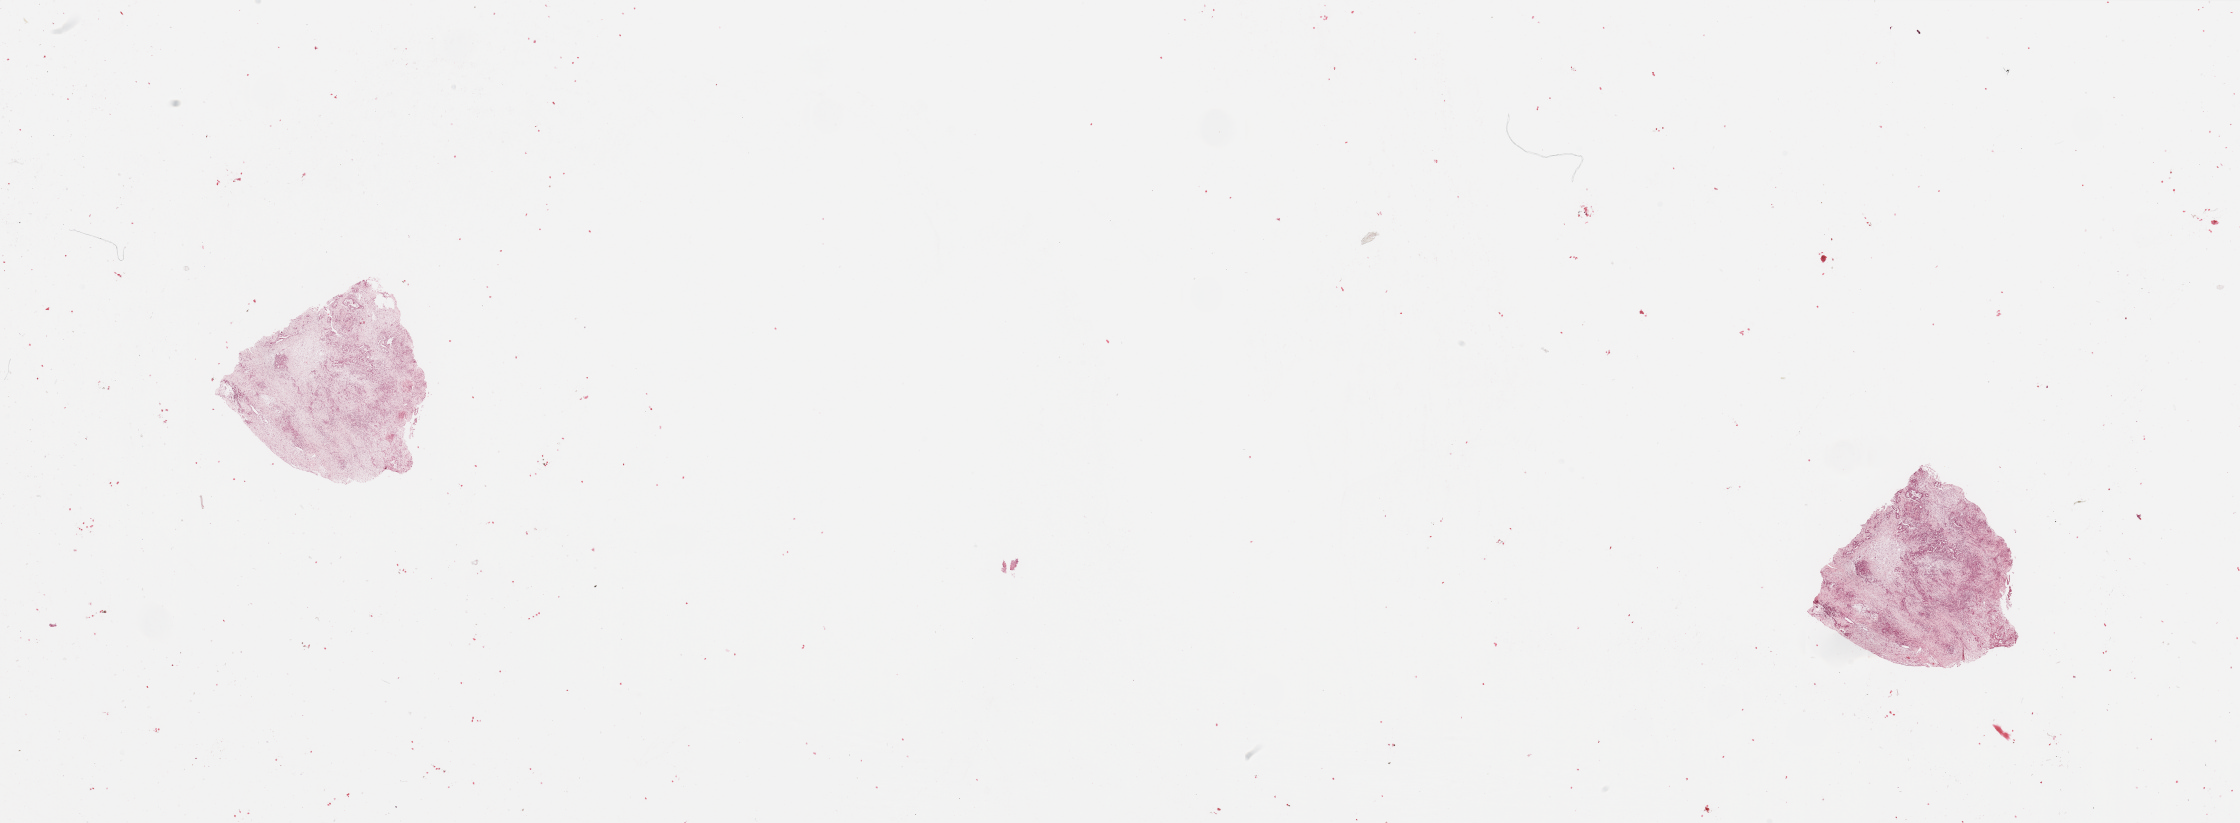
Digitized Hematoxylin and eosin (H&E) stained tissue section (whole slide), low-resolution overview of the scanned area, about 35.4 x 13.0 mm. Tumour tissue sample, sampled site: pancreas. Female, 54 y/o. Histologic grade: G2 (moderately differentiated). Pathologist review of this section (percent, as recorded): tumour nuclei 20%, necrosis 0%.
* primary tumour site (as recorded): head
* diagnosis: Infiltrating duct carcinoma, NOS